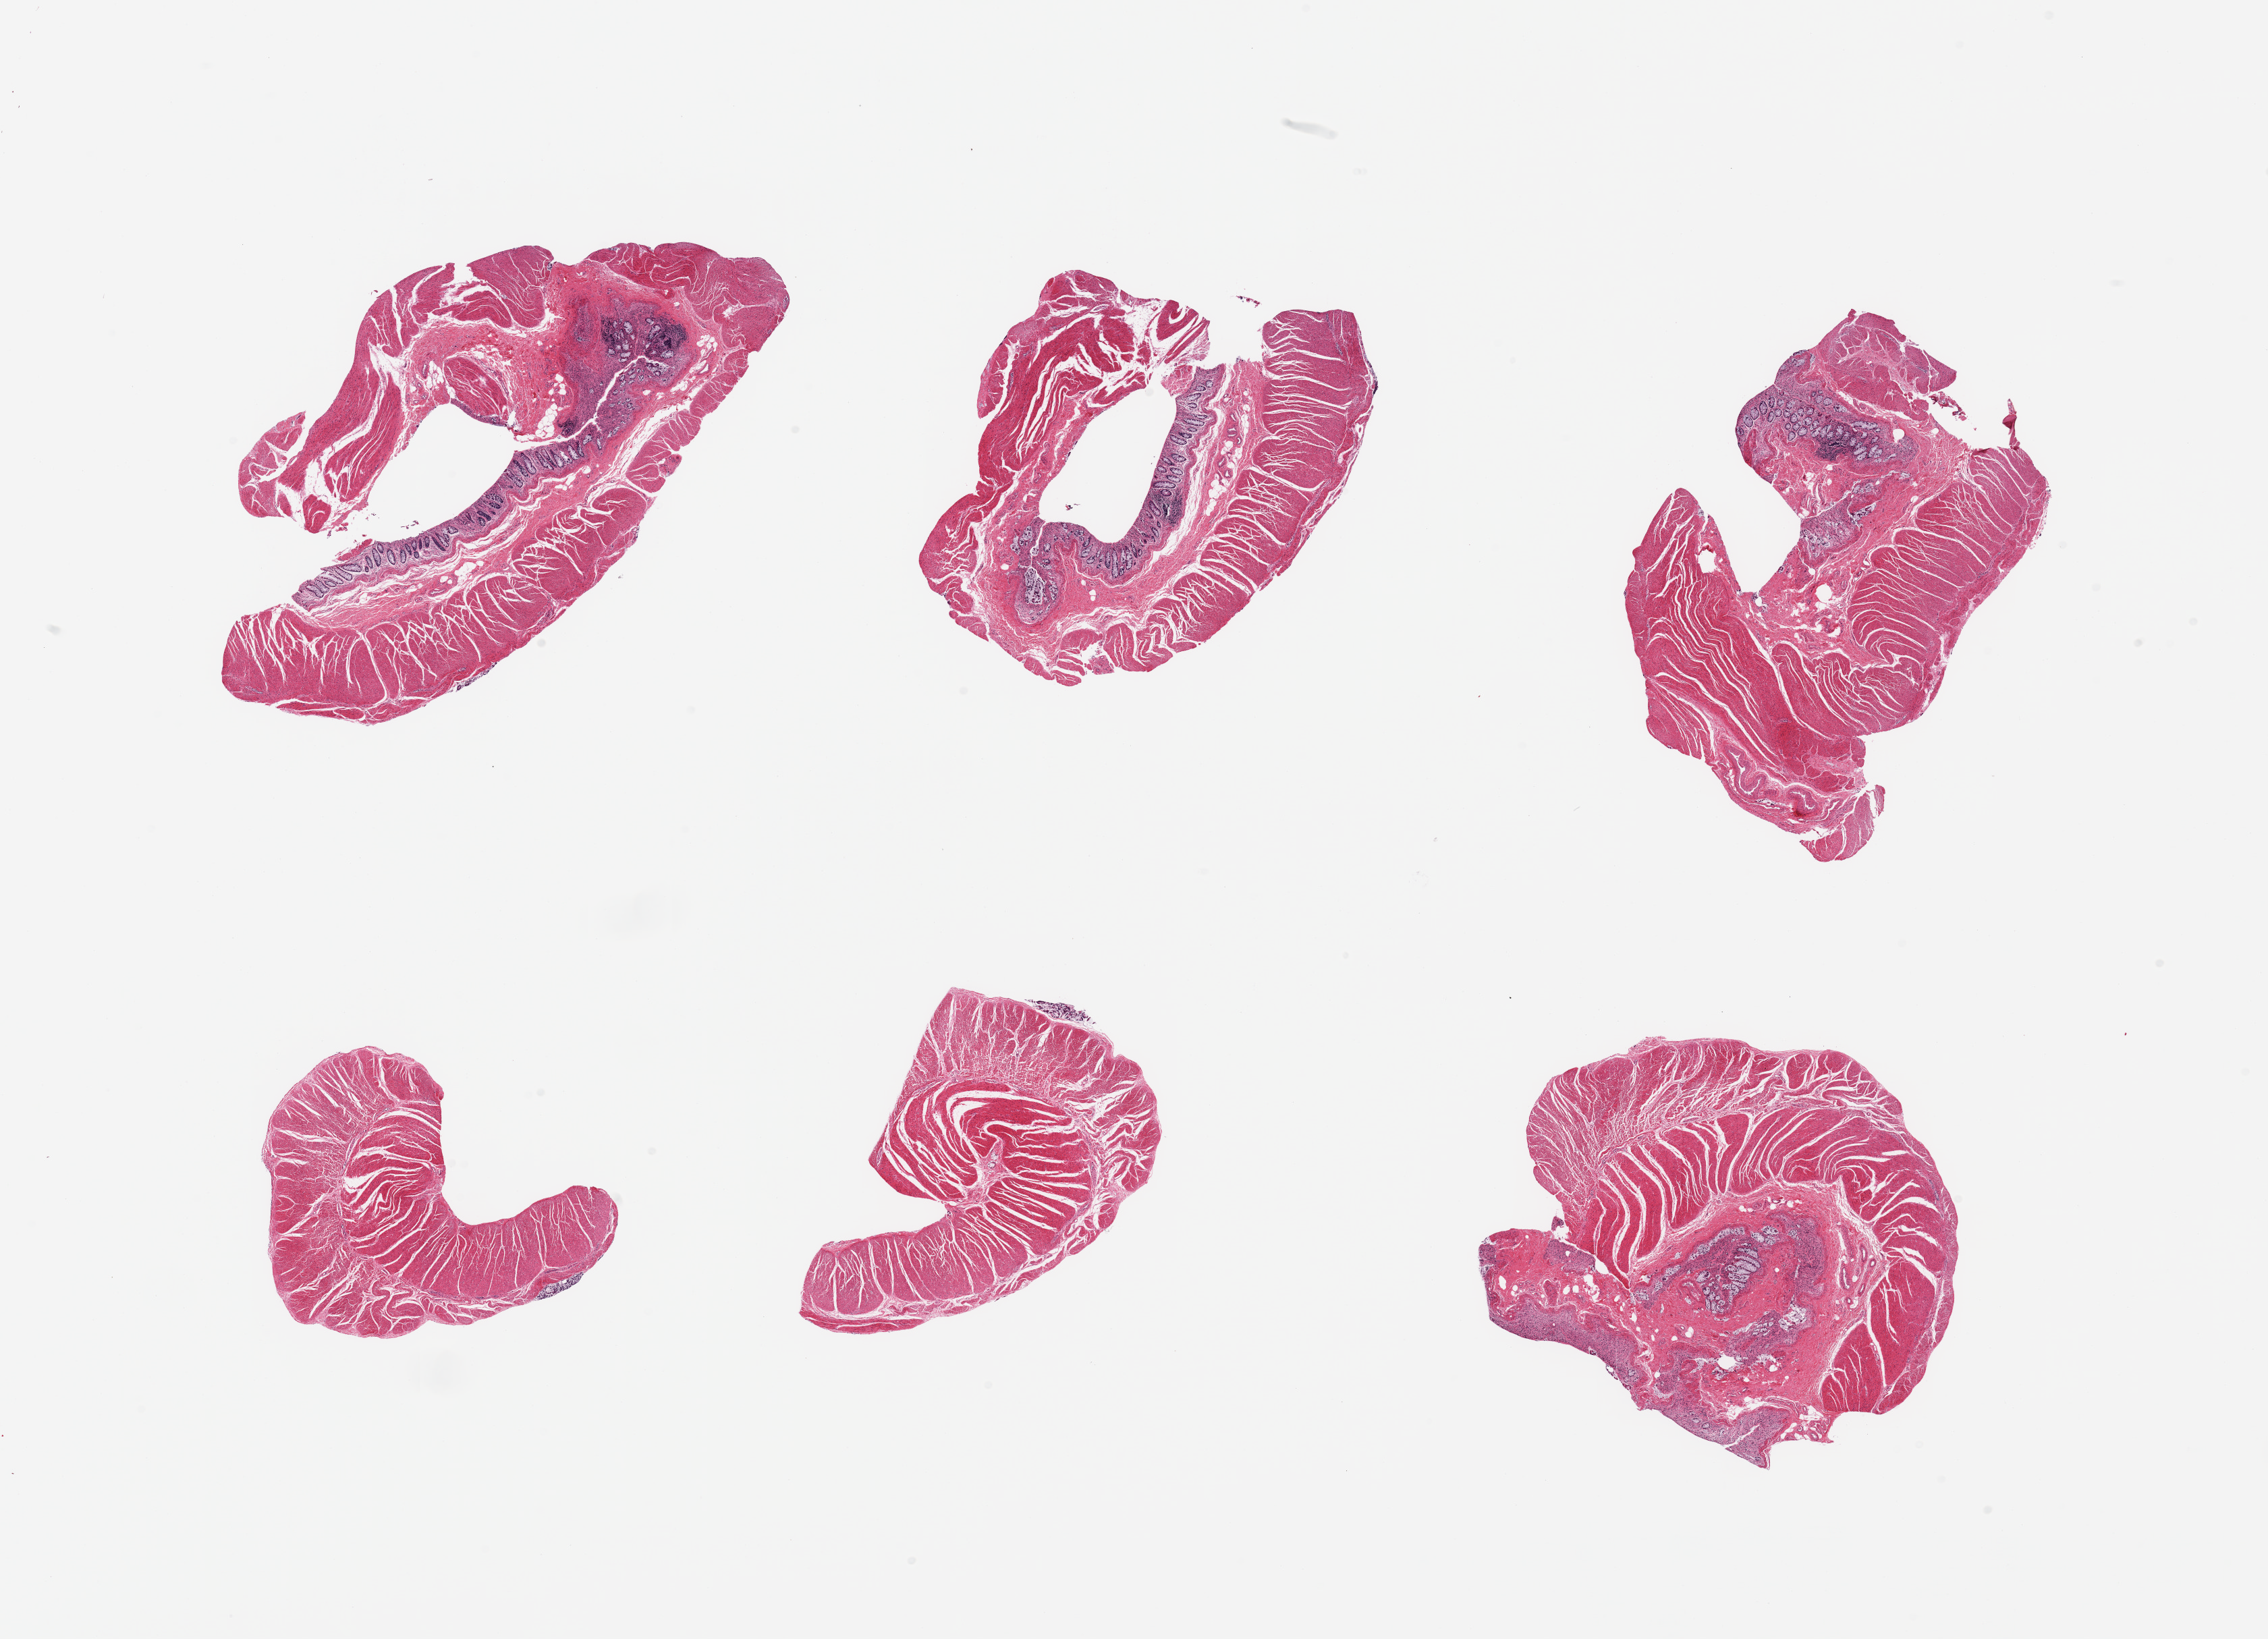
Whole-slide image, haematoxylin and eosin stain, brightfield, shown as a low-resolution overview of the whole scanned area (about 26.6 x 19.2 mm, acquisition: 20x scan). PAXgene-fixed, paraffin-embedded tissue. Section of sigmoid colon (target tissue). Tissue donor sample. Donor: female.
Reviewer comment on this tissue sample: 6 pieces; preserved target muscularis and not target moderaterly to severely autolyzed mucosa.